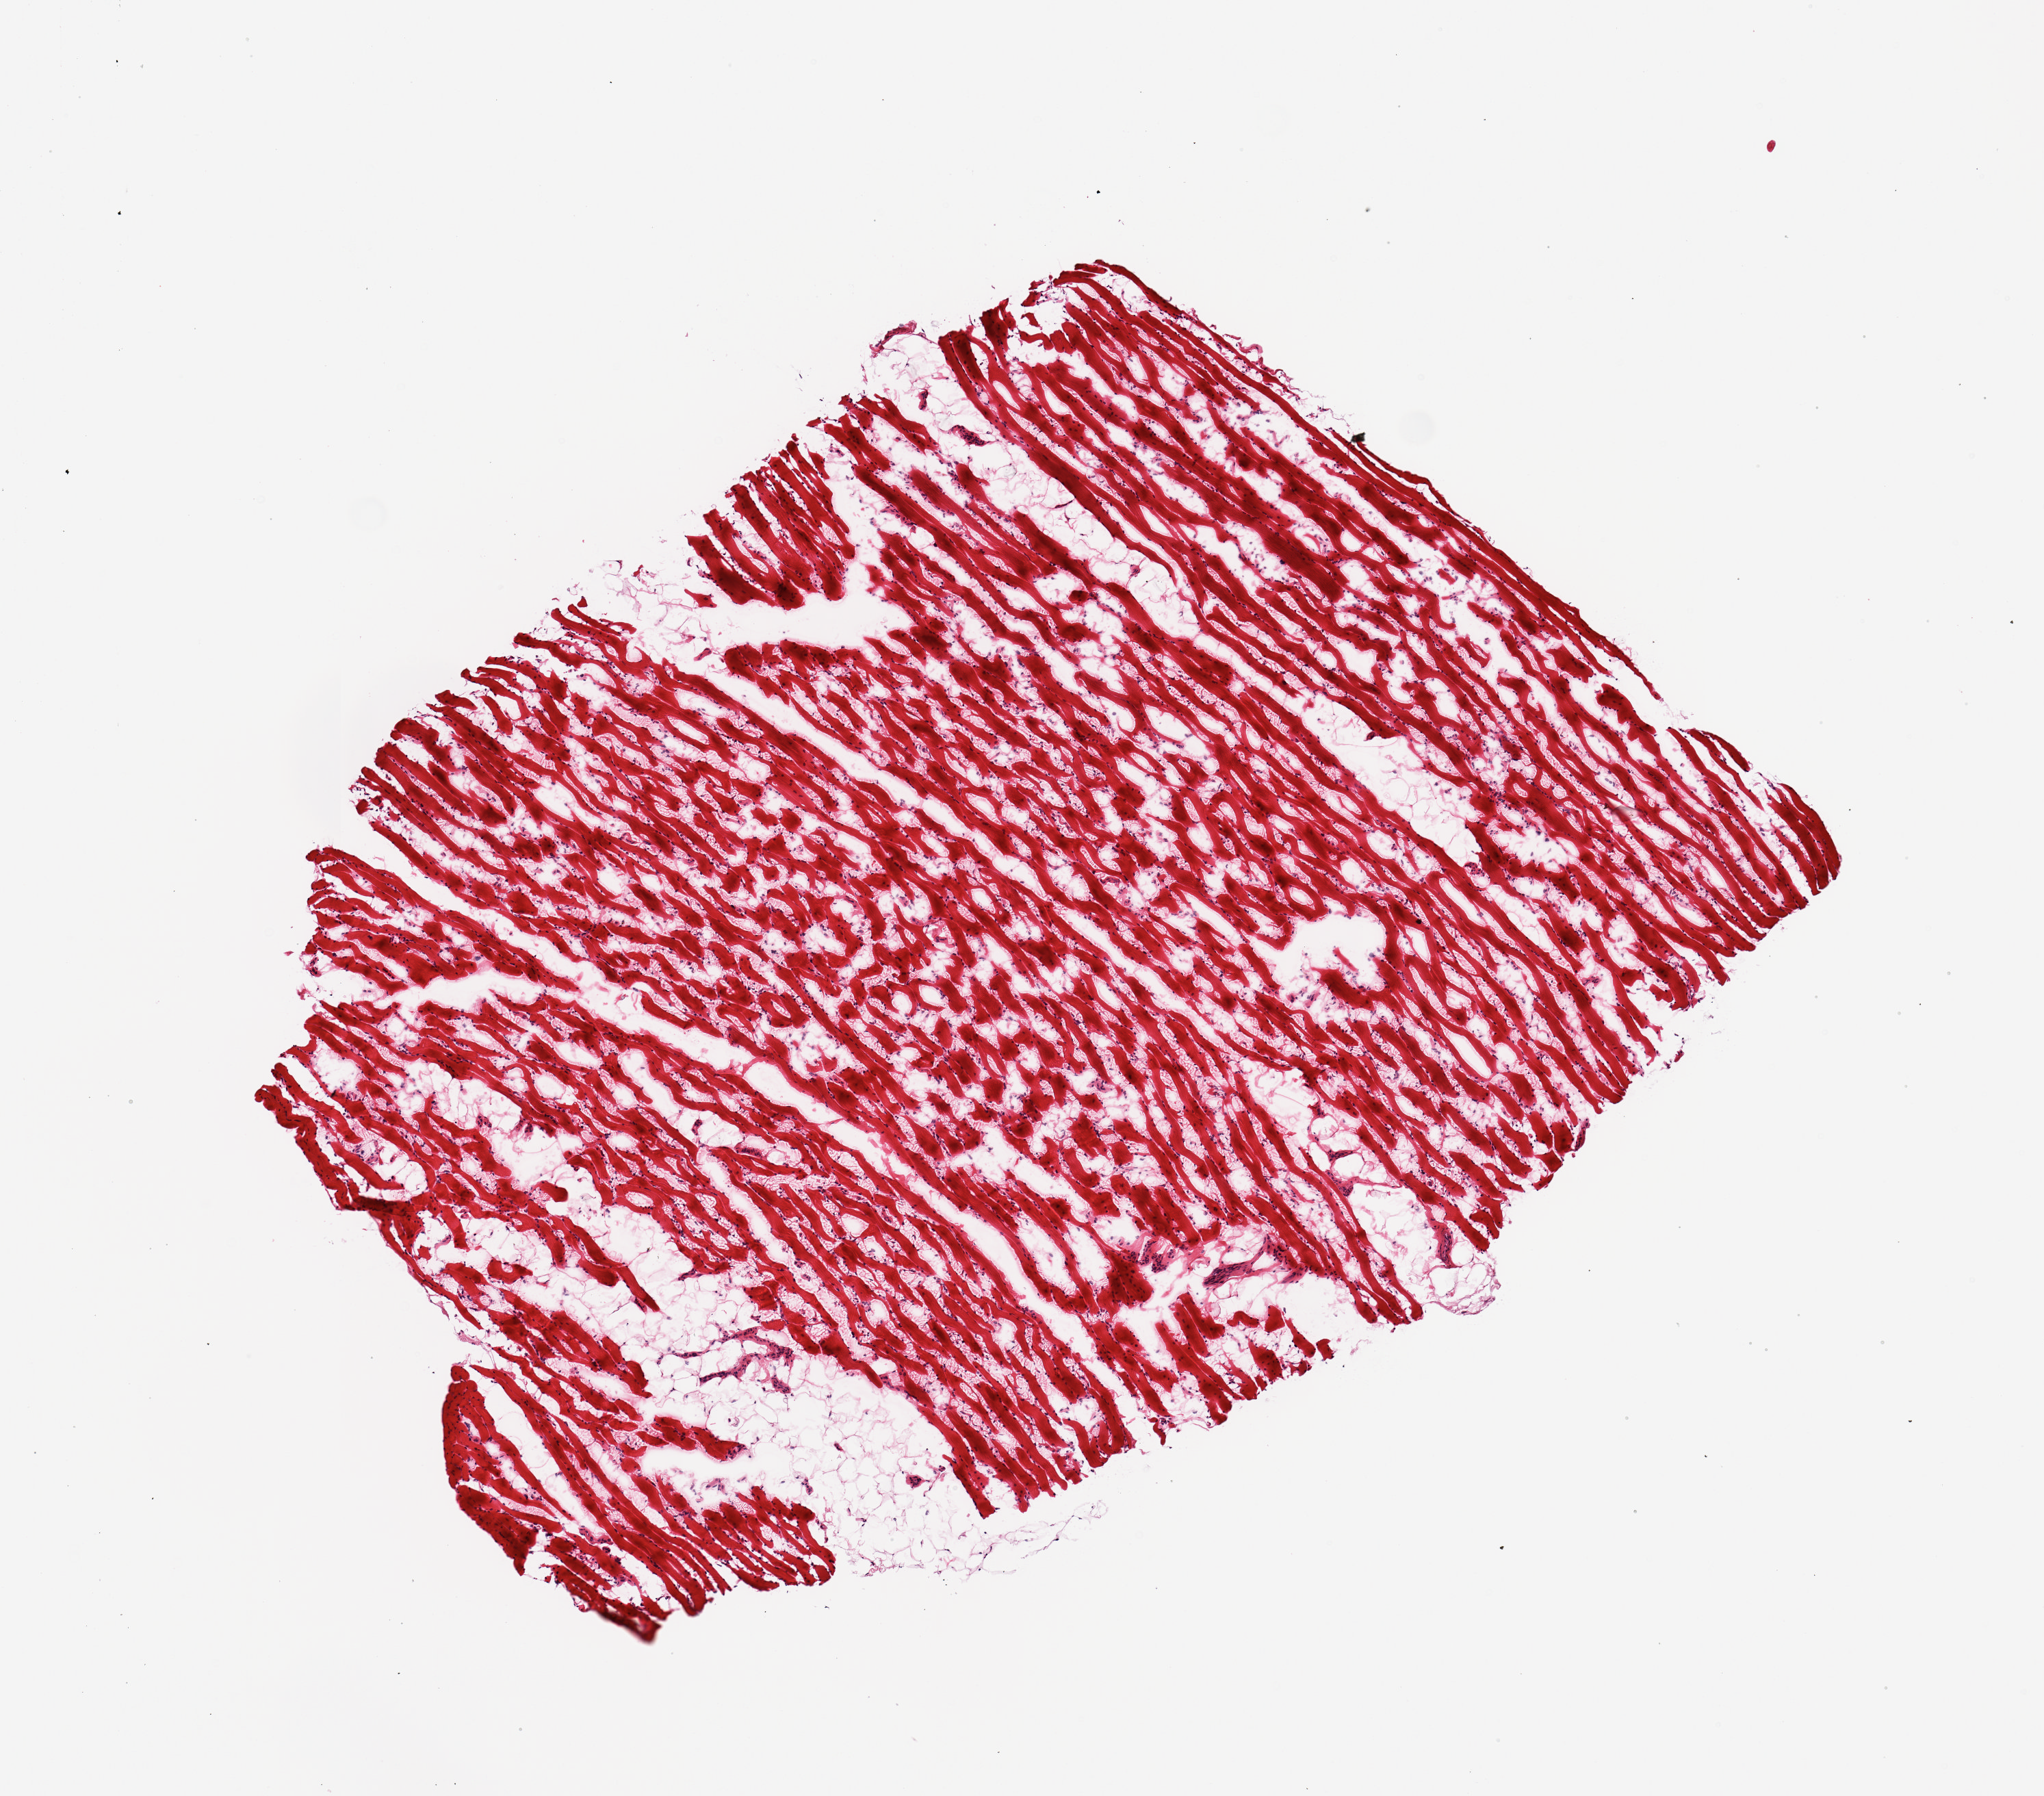
Digitized haematoxylin and eosin-stained section, low-resolution overview of the scanned area, about 5.9 x 5.2 mm; frozen section; target tissue: skeletal muscle; donor tissue sample. Donor sex: female.
Review note (as recorded): 1 piece.